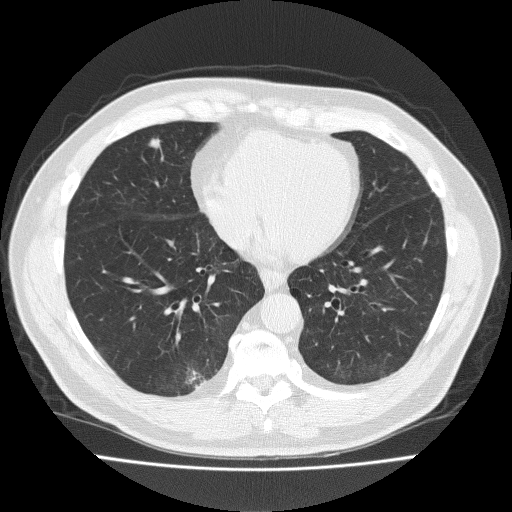
Chest CT (low-dose screening protocol), one axial image. Second screening round (one year after baseline). Lung window (W 1500 / L -600 HU). 2 mm slice thickness. 120 kVp. Male participant, aged 57 years at enrolment. Current smoker at enrolment.
Expert reader's lesion annotation, bounding box (x1, y1, x2, y2) in pixels: (131, 131, 174, 168). Screening reader's record for this exam (one nodule recorded; not confirmed to be the boxed lesion): non-calcified nodule or mass ≥4 mm, right middle lobe, 8 × 7 mm, spiculated (stellate) margins, soft tissue attenuation, pre-existing on the prior screen: yes; interval growth: yes. Later outcome: lung cancer diagnosed 67 days after this screen — adenocarcinoma, NOS, right middle lobe, moderately differentiated (G2), stage IA (AJCC 6th edition), 12 mm at pathology.